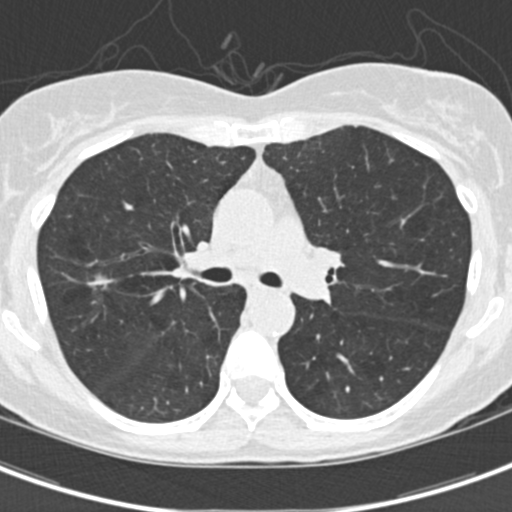
Low-dose screening chest CT, one axial slice. Position 97 of 154 along the scan axis. Lung window (W 1500 / L -600 HU). 2 mm slice thickness. 512 × 512 image matrix, field of view 280 × 280 mm.
Outlined on this slice (manually delineated by an expert):
- lesion 1 (tumor, upper lobe of right lung): bounding box <87,275,109,289> (left, top, right, bottom; pixels)